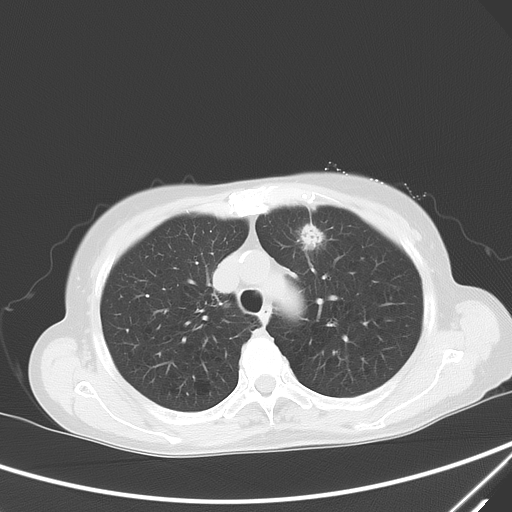
Chest CT, one axial slice; slice 46 of 60 in the series (ordered by position); lung window (W 1500 / L -600 HU); 5 mm slice thickness; 512 × 512 image matrix, field of view 350 × 350 mm. Female patient, age 71 years. From the clinical record (not read from this slice): clinical TNM (as recorded): T1c N0 M0.
Structures marked on this image (bounding box drawn by a radiologist):
- lung tumour (recorded histology: adenocarcinoma): box from (x=295, y=214) to (x=328, y=260) px